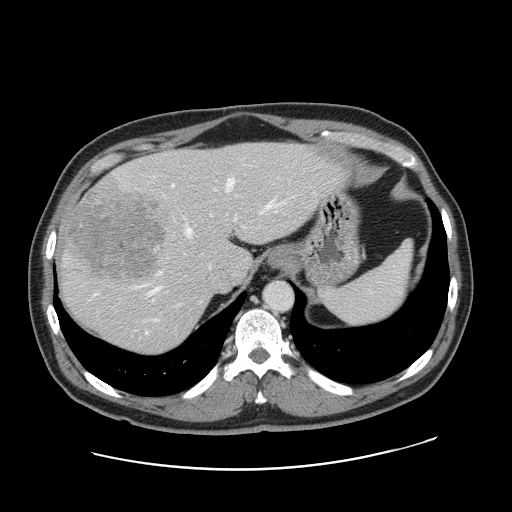
Contrast-enhanced abdominal CT, one axial slice. Position 124 of 178 along the scan axis. 120 kVp. Intravenous contrast given. Soft-tissue window (W 400 / L 40 HU). 512 × 512 image matrix, field of view 403 × 403 mm. Male patient, age 63 years. From the clinical record (not read from this slice): diagnosis: colorectal cancer liver metastases, imaged before liver resection; multiple liver metastases: yes; largest metastasis: 8 cm.
Annotated regions visible in this slice (expert manual segmentation):
- hepatic veins: bounding box (x1, y1, x2, y2) in pixels: (151, 178, 272, 293)
- liver: (59, 142, 342, 354)
- planned liver remnant (the part of the liver to remain after resection): (146, 143, 342, 281)
- portal vein (with intrahepatic branches): (153, 185, 245, 321)
- liver metastasis: (67, 193, 165, 280)